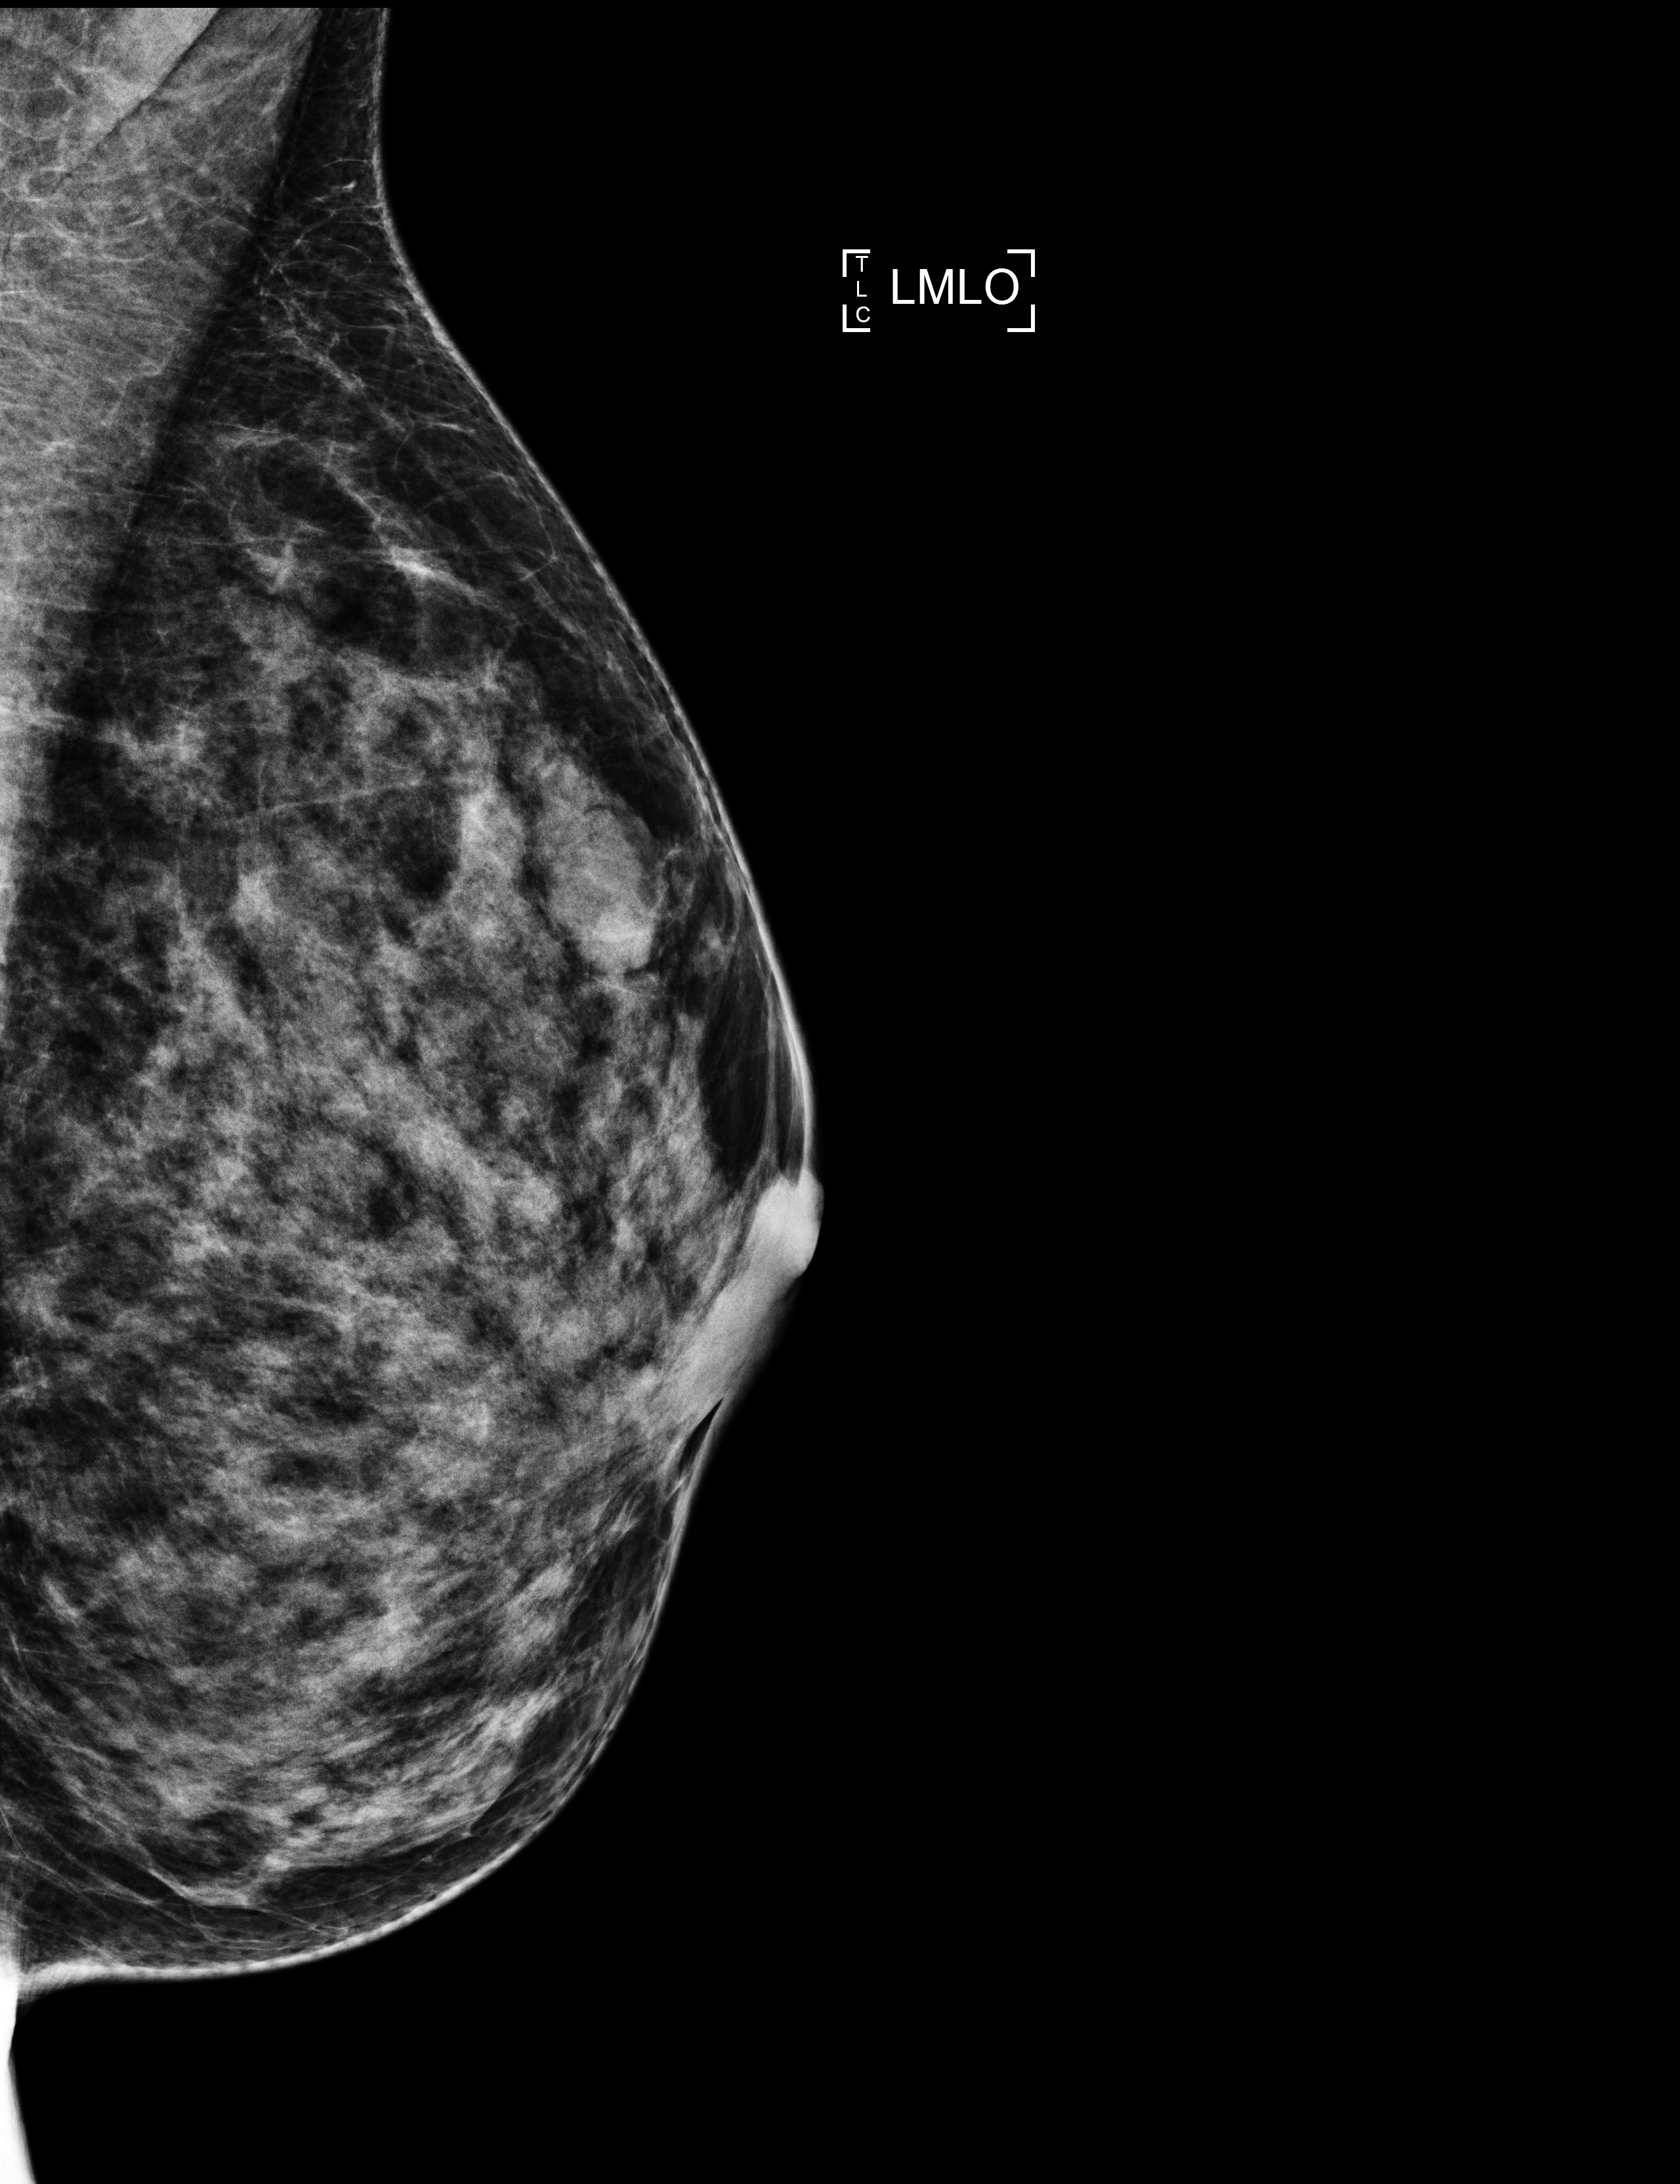
Annual screening mammography examination, compressed breast thickness 41 mm, system: Selenia Dimensions. Female patient, age 53 years.
Image type: full-field digital mammogram. Breast: left. Projection: MLO view.